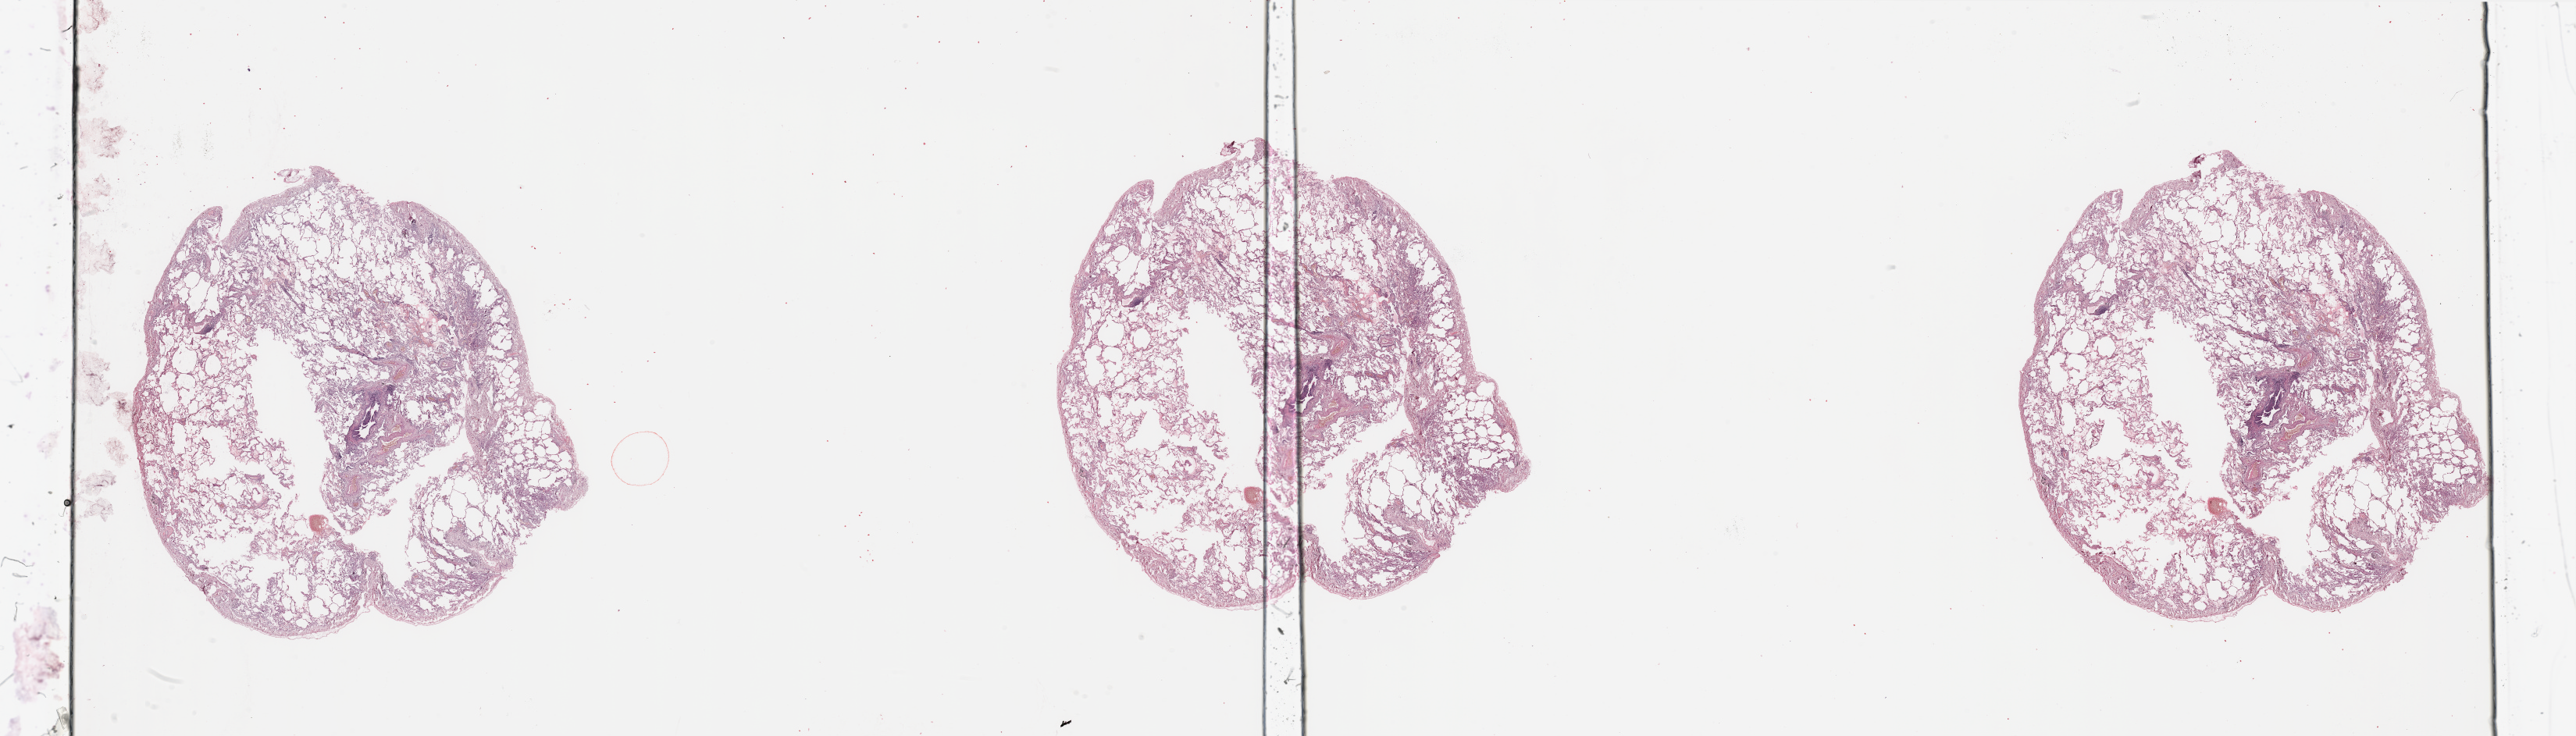
Digitized H&E-stained tissue section (whole slide) — a low-resolution overview of the entire scanned area, about 52.2 x 14.9 mm (acquisition: 20x scan), normal (non-tumour) tissue sample, sampled site: lung. Patient: male, age 51 years.
This section: normal (non-tumour) tissue from the same patient. Patient diagnosis: Adenocarcinoma, NOS.